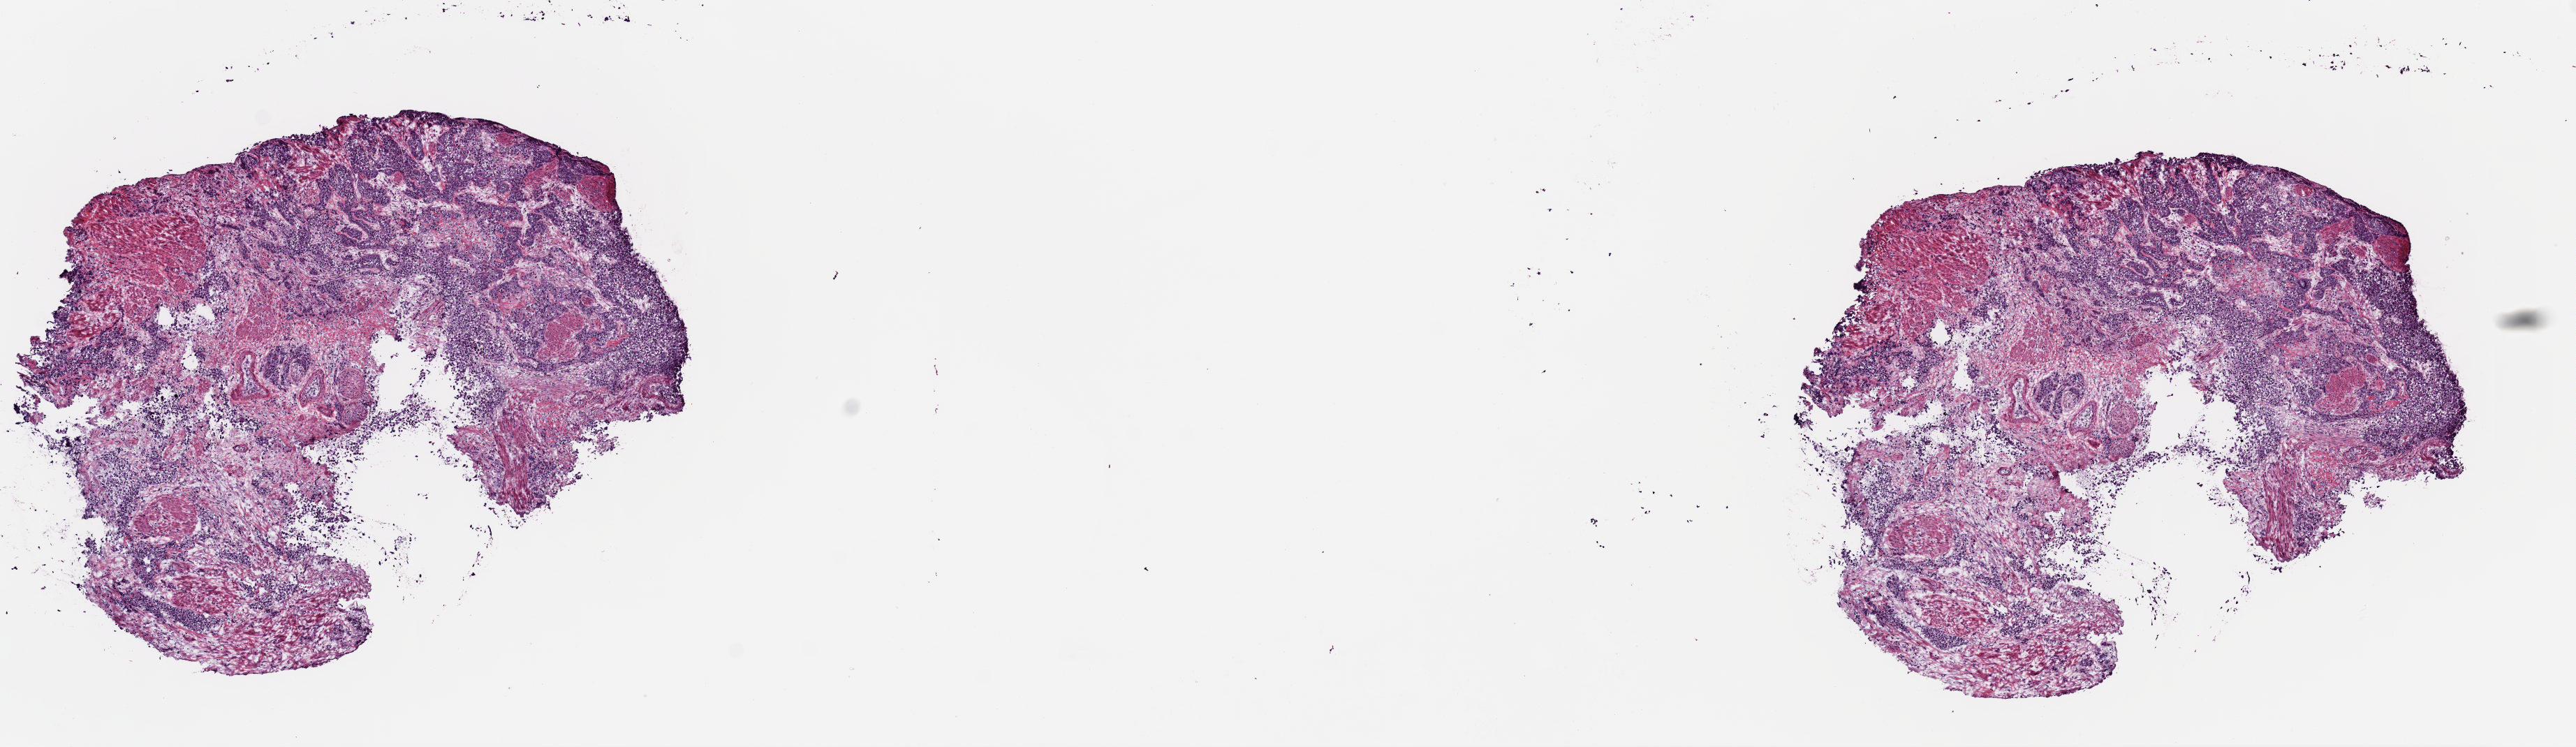
Whole-slide histology image, H&E — low-resolution overview of the scanned area, about 14.6 x 4.2 mm. Frozen section. Bladder, primary tumour sample. Patient: female, age at initial diagnosis 53 years. Histologic grade: high grade. Slide review estimates, as recorded: tumour cells 50%, tumour nuclei 85%, normal cells 0%, stromal cells 45%, necrosis 5%. Inflammatory infiltration, as recorded: lymphocyte infiltration 1%, monocyte infiltration 0%, neutrophil infiltration 0%.
- lymph nodes positive (case pathology): 2 of 17 examined
- histologic diagnosis: Transitional cell carcinoma
- AJCC pathologic stage: IV